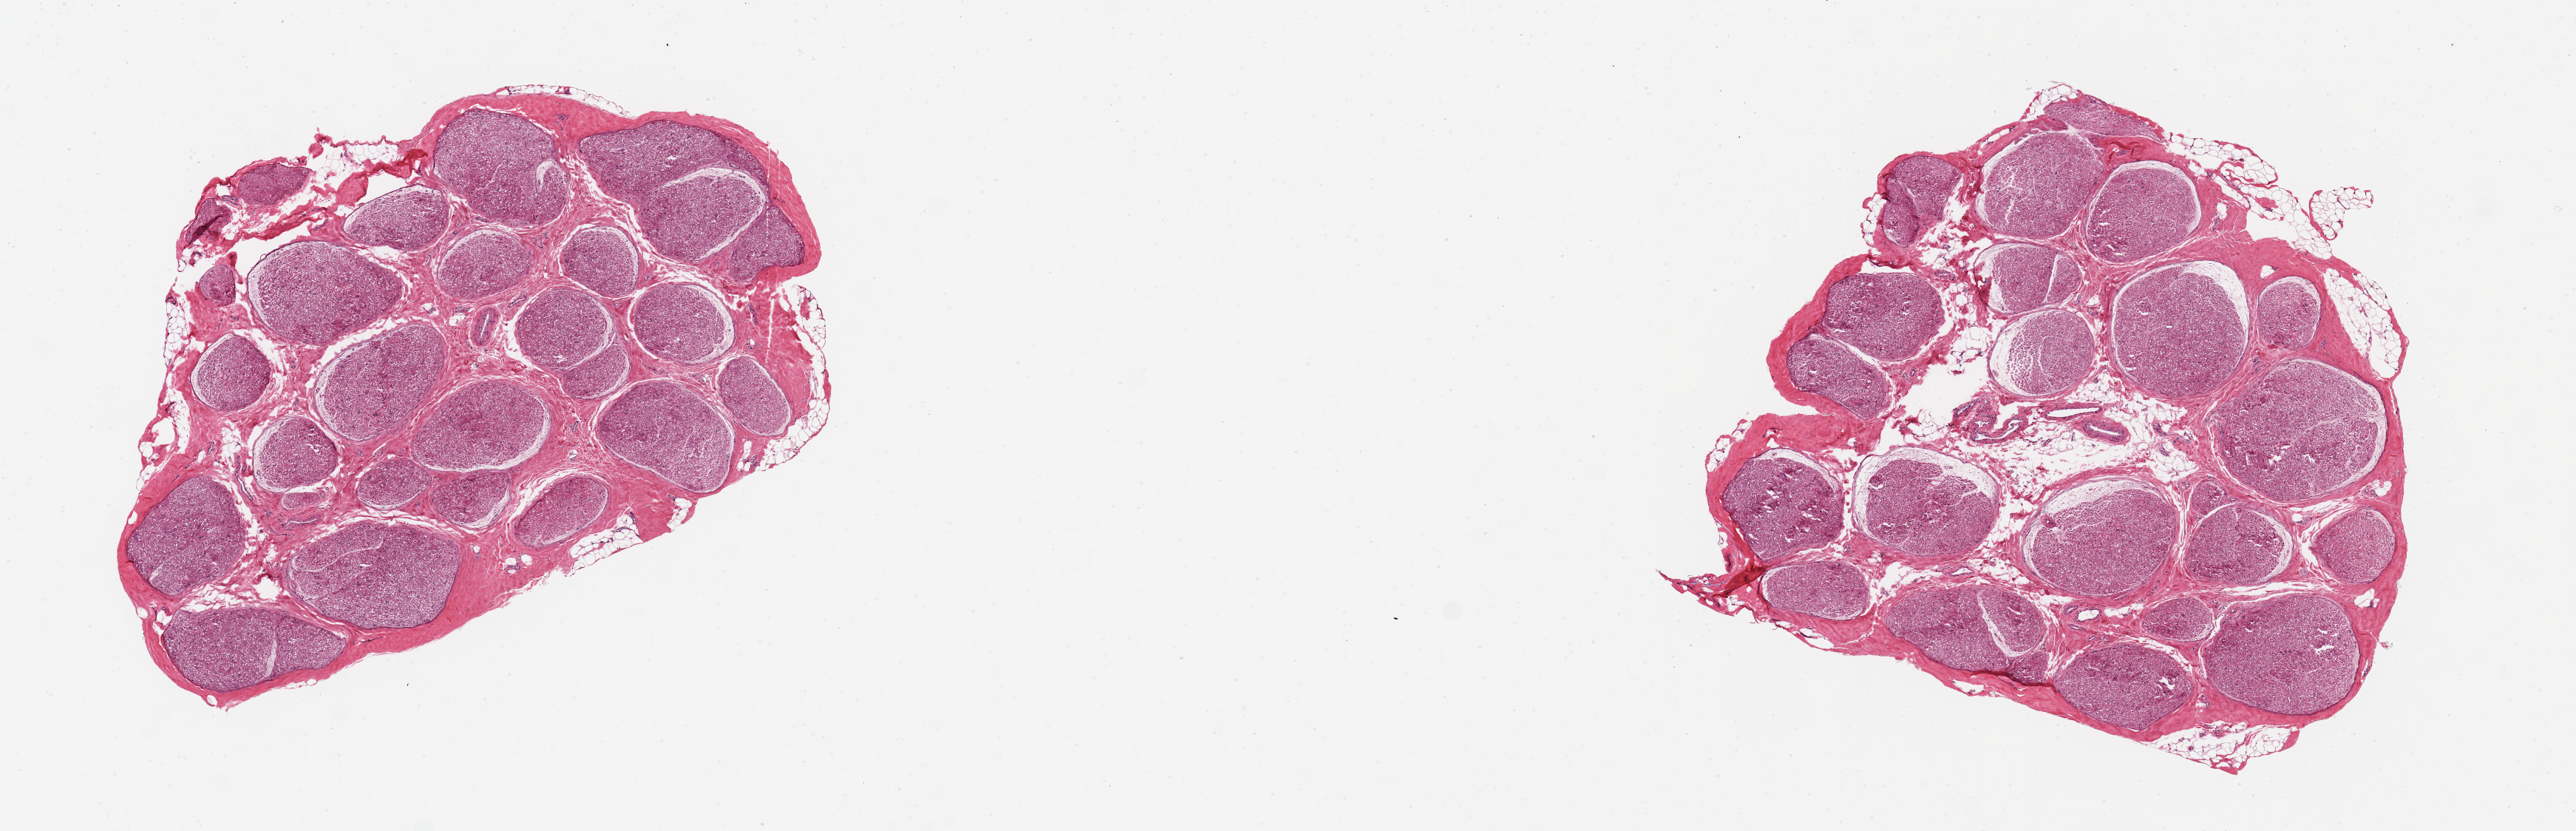
Digitized H&E-stained section — shown as a low-resolution overview of the whole scanned area (about 13.8 x 4.4 mm, slide scanned at 20x); PAXgene-fixed paraffin-embedded (PFPE) section; sampled site (target tissue): tibial nerve; tissue donor sample. Male donor.
Pathologist's review note for this sample: 2 pieces, 2.5x4 & 2.5x3 mm, minimal peripheral adipose.